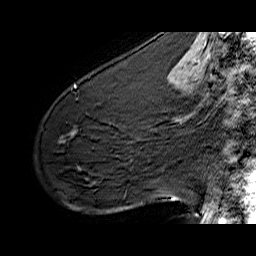
Breast MRI (dynamic contrast-enhanced), one sagittal slice. Position 37 of 60 along the scan axis. Dynamic contrast-enhanced series, time point 2 of 6 at this slice position (early post-contrast). 1.5 T. TE 6.4 ms, TR 32.9 ms. 4 mm slice thickness. 256 × 256 image matrix, field of view 200 × 200 mm. Female patient. From the clinical record (not read from this slice): setting: breast cancer imaged before/during neoadjuvant chemotherapy; receptor status: HER2-positive.
Structures marked on this image (semi-automatically segmented with operator editing):
- analysis volume of interest (the breast-tissue region the enhancement analysis was run in; not a lesion): bounding box <61,77,141,142> (left, top, right, bottom; pixels)
- tumour enhancement mask (voxels above the 100 % enhancement threshold inside the analysis volume of interest): <74,85,76,87>